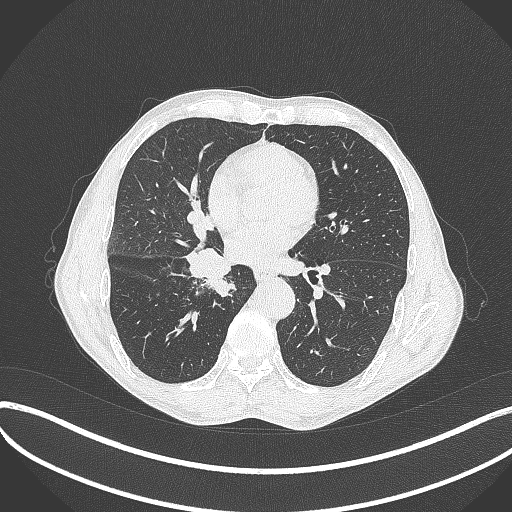
Chest CT, one axial slice. 120 kVp. Lung window (W 1500 / L -600 HU). 1 mm slice thickness. 512 × 512 image matrix, field of view 400 × 400 mm. Patient: male, 65 years. From the clinical record (not read from this slice): clinical TNM (as recorded): T2a N0 M0.
Structures marked on this image (bounding box drawn by a radiologist):
- lung tumour (recorded histology: squamous cell carcinoma): box from (x=180, y=239) to (x=238, y=298) px